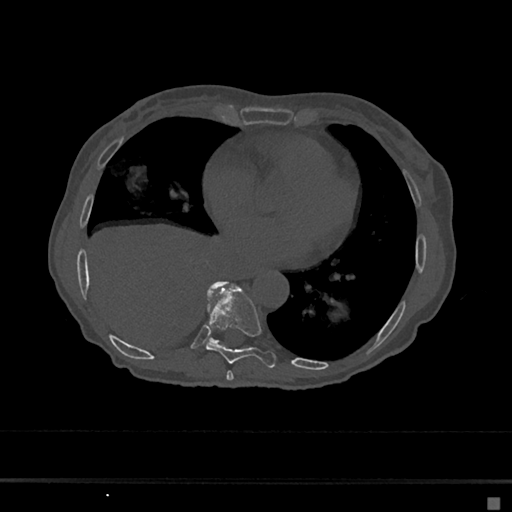
CT including the spine, one axial slice; slice 315 of 797 in the series (ordered by position); reconstruction kernel Br40s/3; 120 kVp; bone window (W 1800 / L 400 HU); 0.5 mm slice thickness; 512 × 512 image matrix. Patient: female, 68 years. Case-level facts recorded for this patient, not image findings: primary cancer: renal.
Outlined on this slice (semi-automatically segmented with operator editing):
- T7 vertebra: bounding box <226,371,234,381> (left, top, right, bottom; pixels)
- T8 vertebra: <206,284,276,368>
- T9 vertebra: <209,281,226,343>